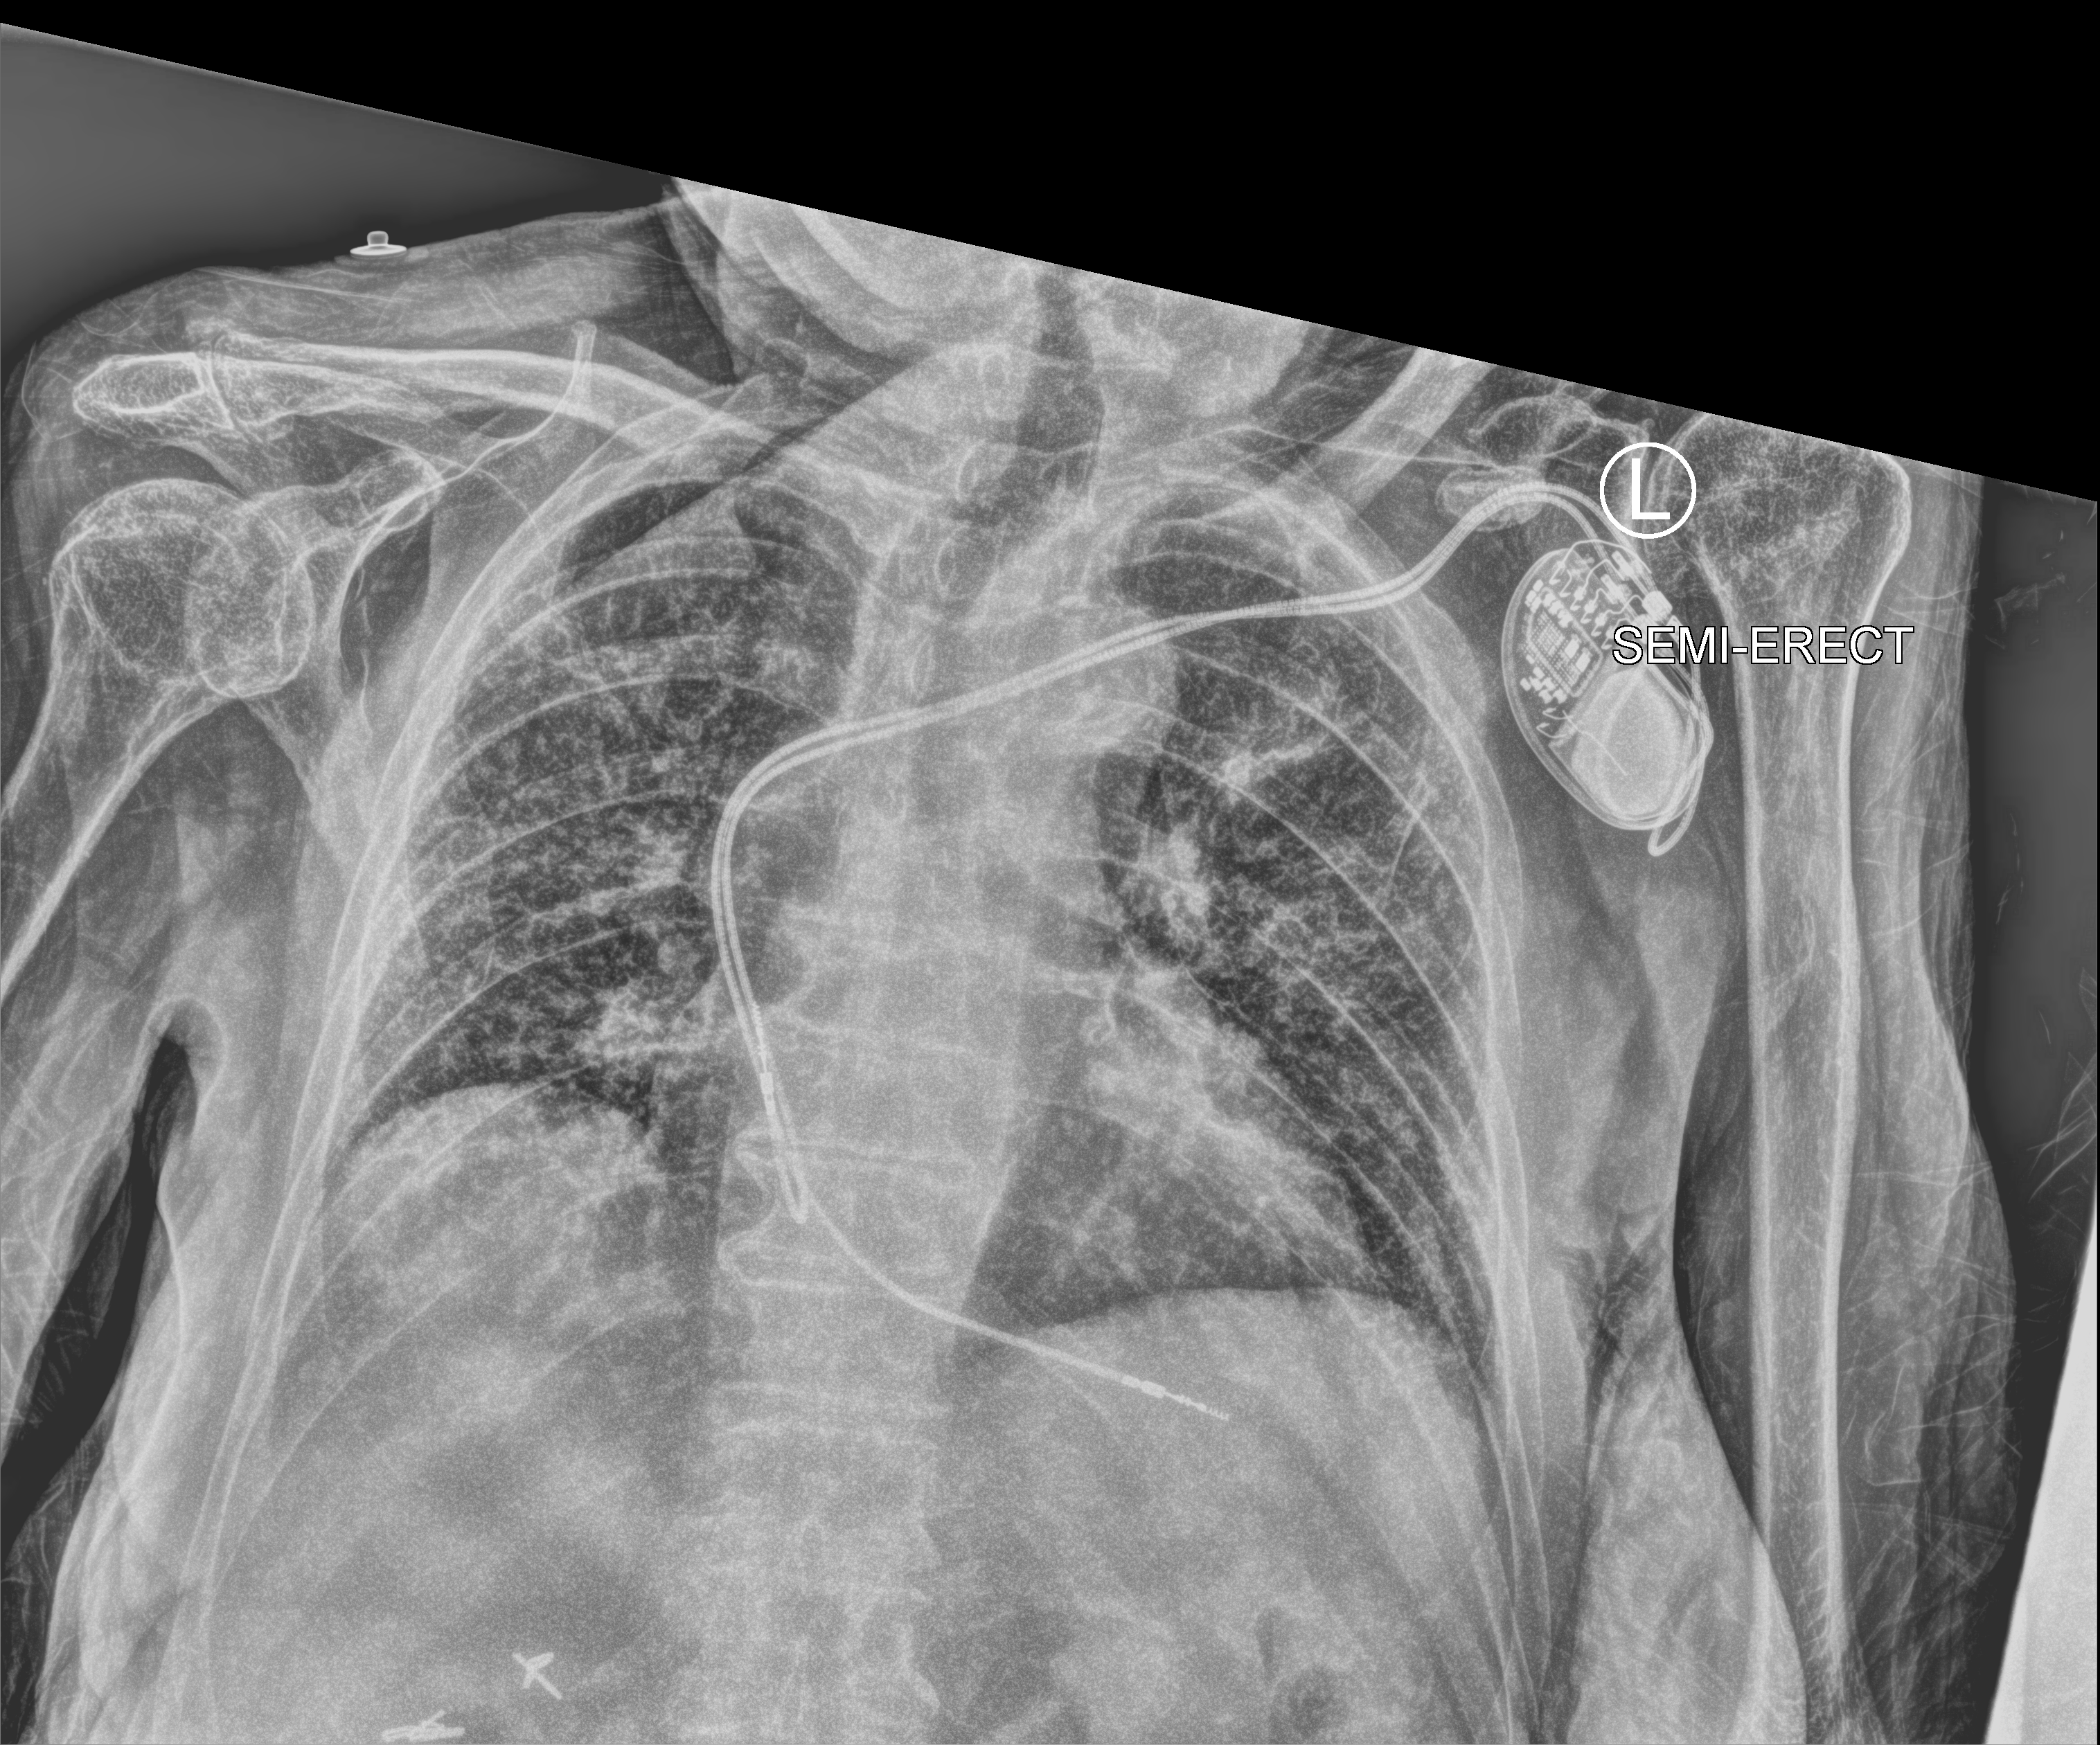
Bedside chest radiograph (computed radiography), anteroposterior (AP) projection. Female patient hospitalised with COVID-19, age 75–90 years.
Admission-level facts for this patient (not findings on this image; timing relative to this image not recorded):
- admitted to intensive care during this hospital stay: no